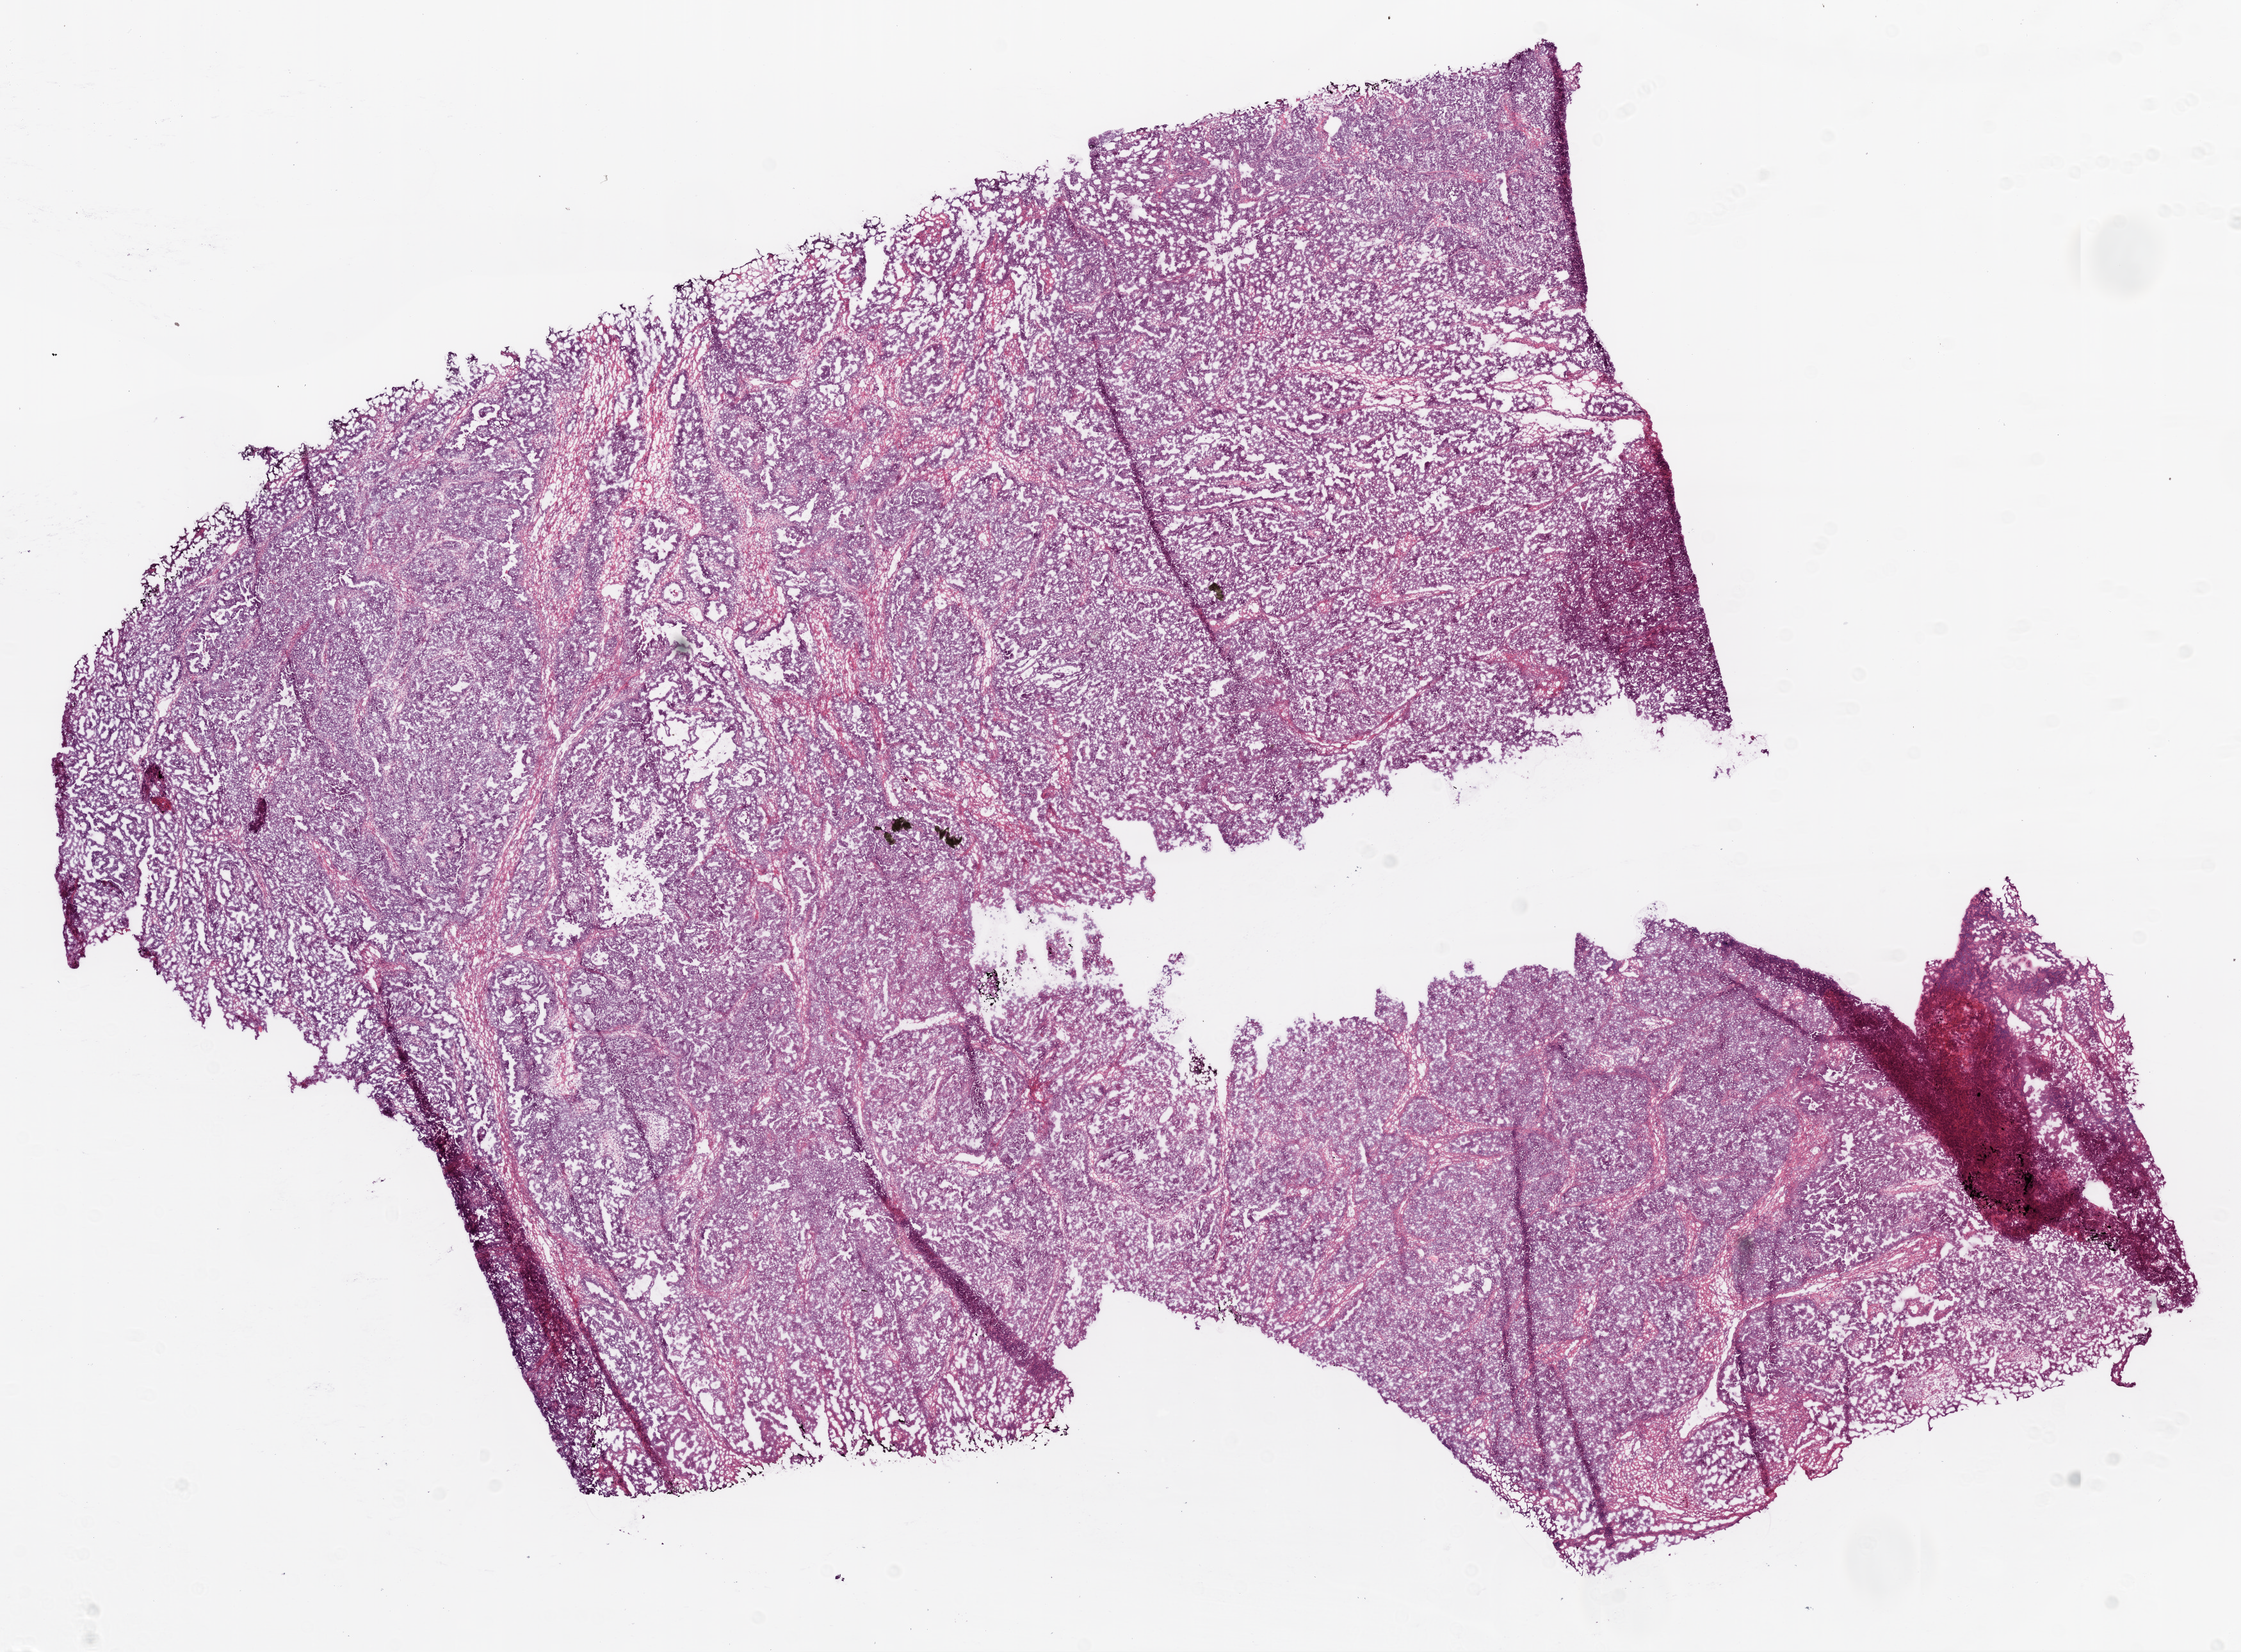
Digitized H&E tissue section (whole slide) — low-resolution overview of the scanned area, about 14.0 x 10.4 mm (acquisition: 20x scan), frozen section from the bottom of the tissue portion, primary tumour sample from the ovary. Patient: female, age at initial diagnosis 66 years. Histologic grade: G3 (poorly differentiated). Pathologist review of this section (percent, as recorded): tumour cells 95%, tumour nuclei 90%, normal cells 0%, stromal cells 5%, necrosis 0%.
Diagnosis: Serous cystadenocarcinoma, NOS. FIGO stage: IIIC.